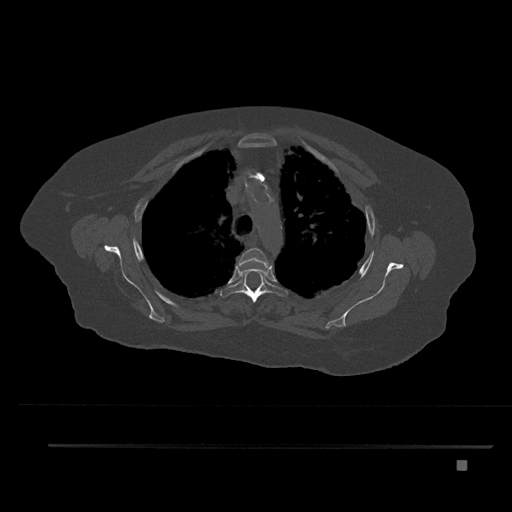
CT including the spine, one axial slice. Slice 611 of 797 in the series (ordered by position). Bone window (W 1800 / L 400 HU). 0.5 mm slice thickness. 512 × 512 image matrix, field of view 437 × 437 mm. Patient: female, 76 years. From the clinical record (not read from this slice): primary cancer: lung.
Structures marked on this image (semi-automatically segmented with operator editing):
- T3 vertebra: bounding box <238,248,270,268> (left, top, right, bottom; pixels)
- T4 vertebra: <220,260,289,302>